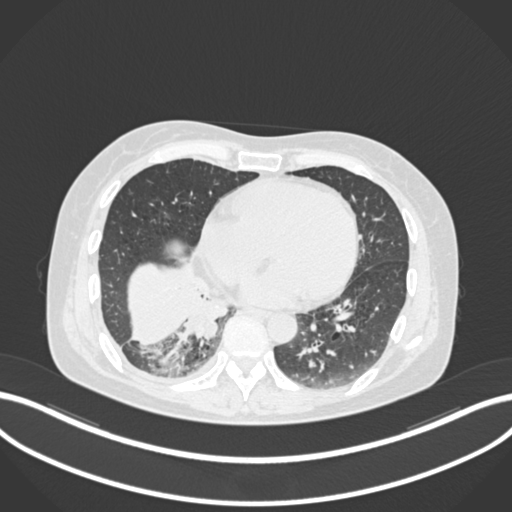
Chest CT, one axial slice. Slice 54 of 168 in the series (ordered by position). Reconstruction kernel B30f. Lung window (W 1500 / L -600 HU). 1 mm slice thickness. 512 × 512 image matrix, field of view 400 × 400 mm. Female patient, age 63 years. From the clinical record (not read from this slice): clinical TNM (as recorded): T1c N0 M0.
Outlined on this slice (rectangle marked by the reading radiologist):
- lung tumour (recorded histology: adenocarcinoma): box from (x=182, y=280) to (x=232, y=345) px